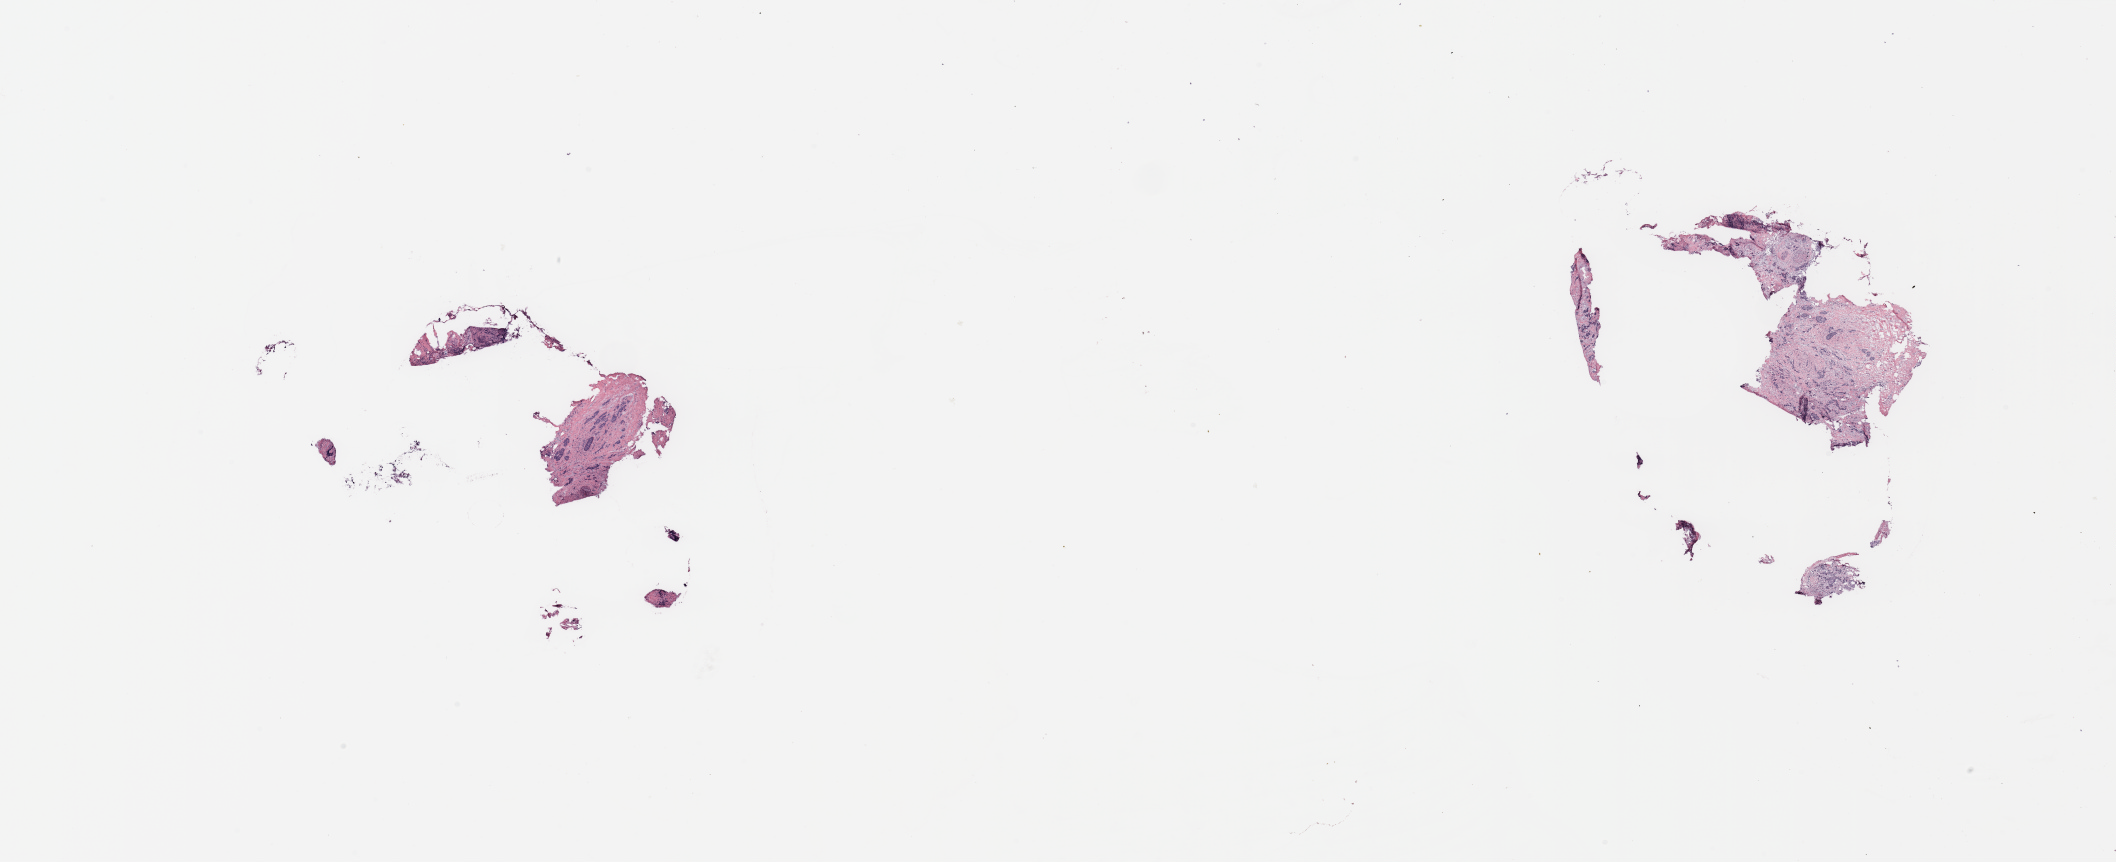
Digitized H&E-stained tissue section (whole slide) — whole scanned area (about 33.5 x 13.6 mm) shown as a low-resolution overview. Breast, tissue type not recorded.
- patient diagnosis (cohort enrolment): breast cancer (breast)